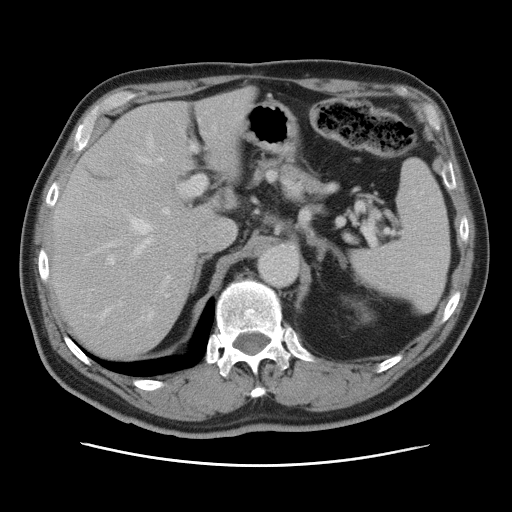
Contrast-enhanced abdominal CT, one axial slice; slice 53 of 80 in the series (ordered by position); intravenous contrast given; soft-tissue window (W 400 / L 40 HU); 5 mm slice thickness; 512 × 512 image matrix, field of view 370 × 370 mm. Male patient, age 69 years. Case-level facts recorded for this patient, not image findings: diagnosis: colorectal cancer liver metastases, imaged before liver resection; multiple liver metastases: no; largest metastasis: 5 cm; disease in both lobes: yes.
Structures marked on this image (manually delineated by an expert):
- hepatic veins: bounding box [x1, y1, x2, y2] px = [97, 141, 164, 320]
- liver: [53, 91, 252, 360]
- planned liver remnant (the part of the liver to remain after resection): [52, 91, 251, 359]
- portal vein (with intrahepatic branches): [107, 119, 216, 293]